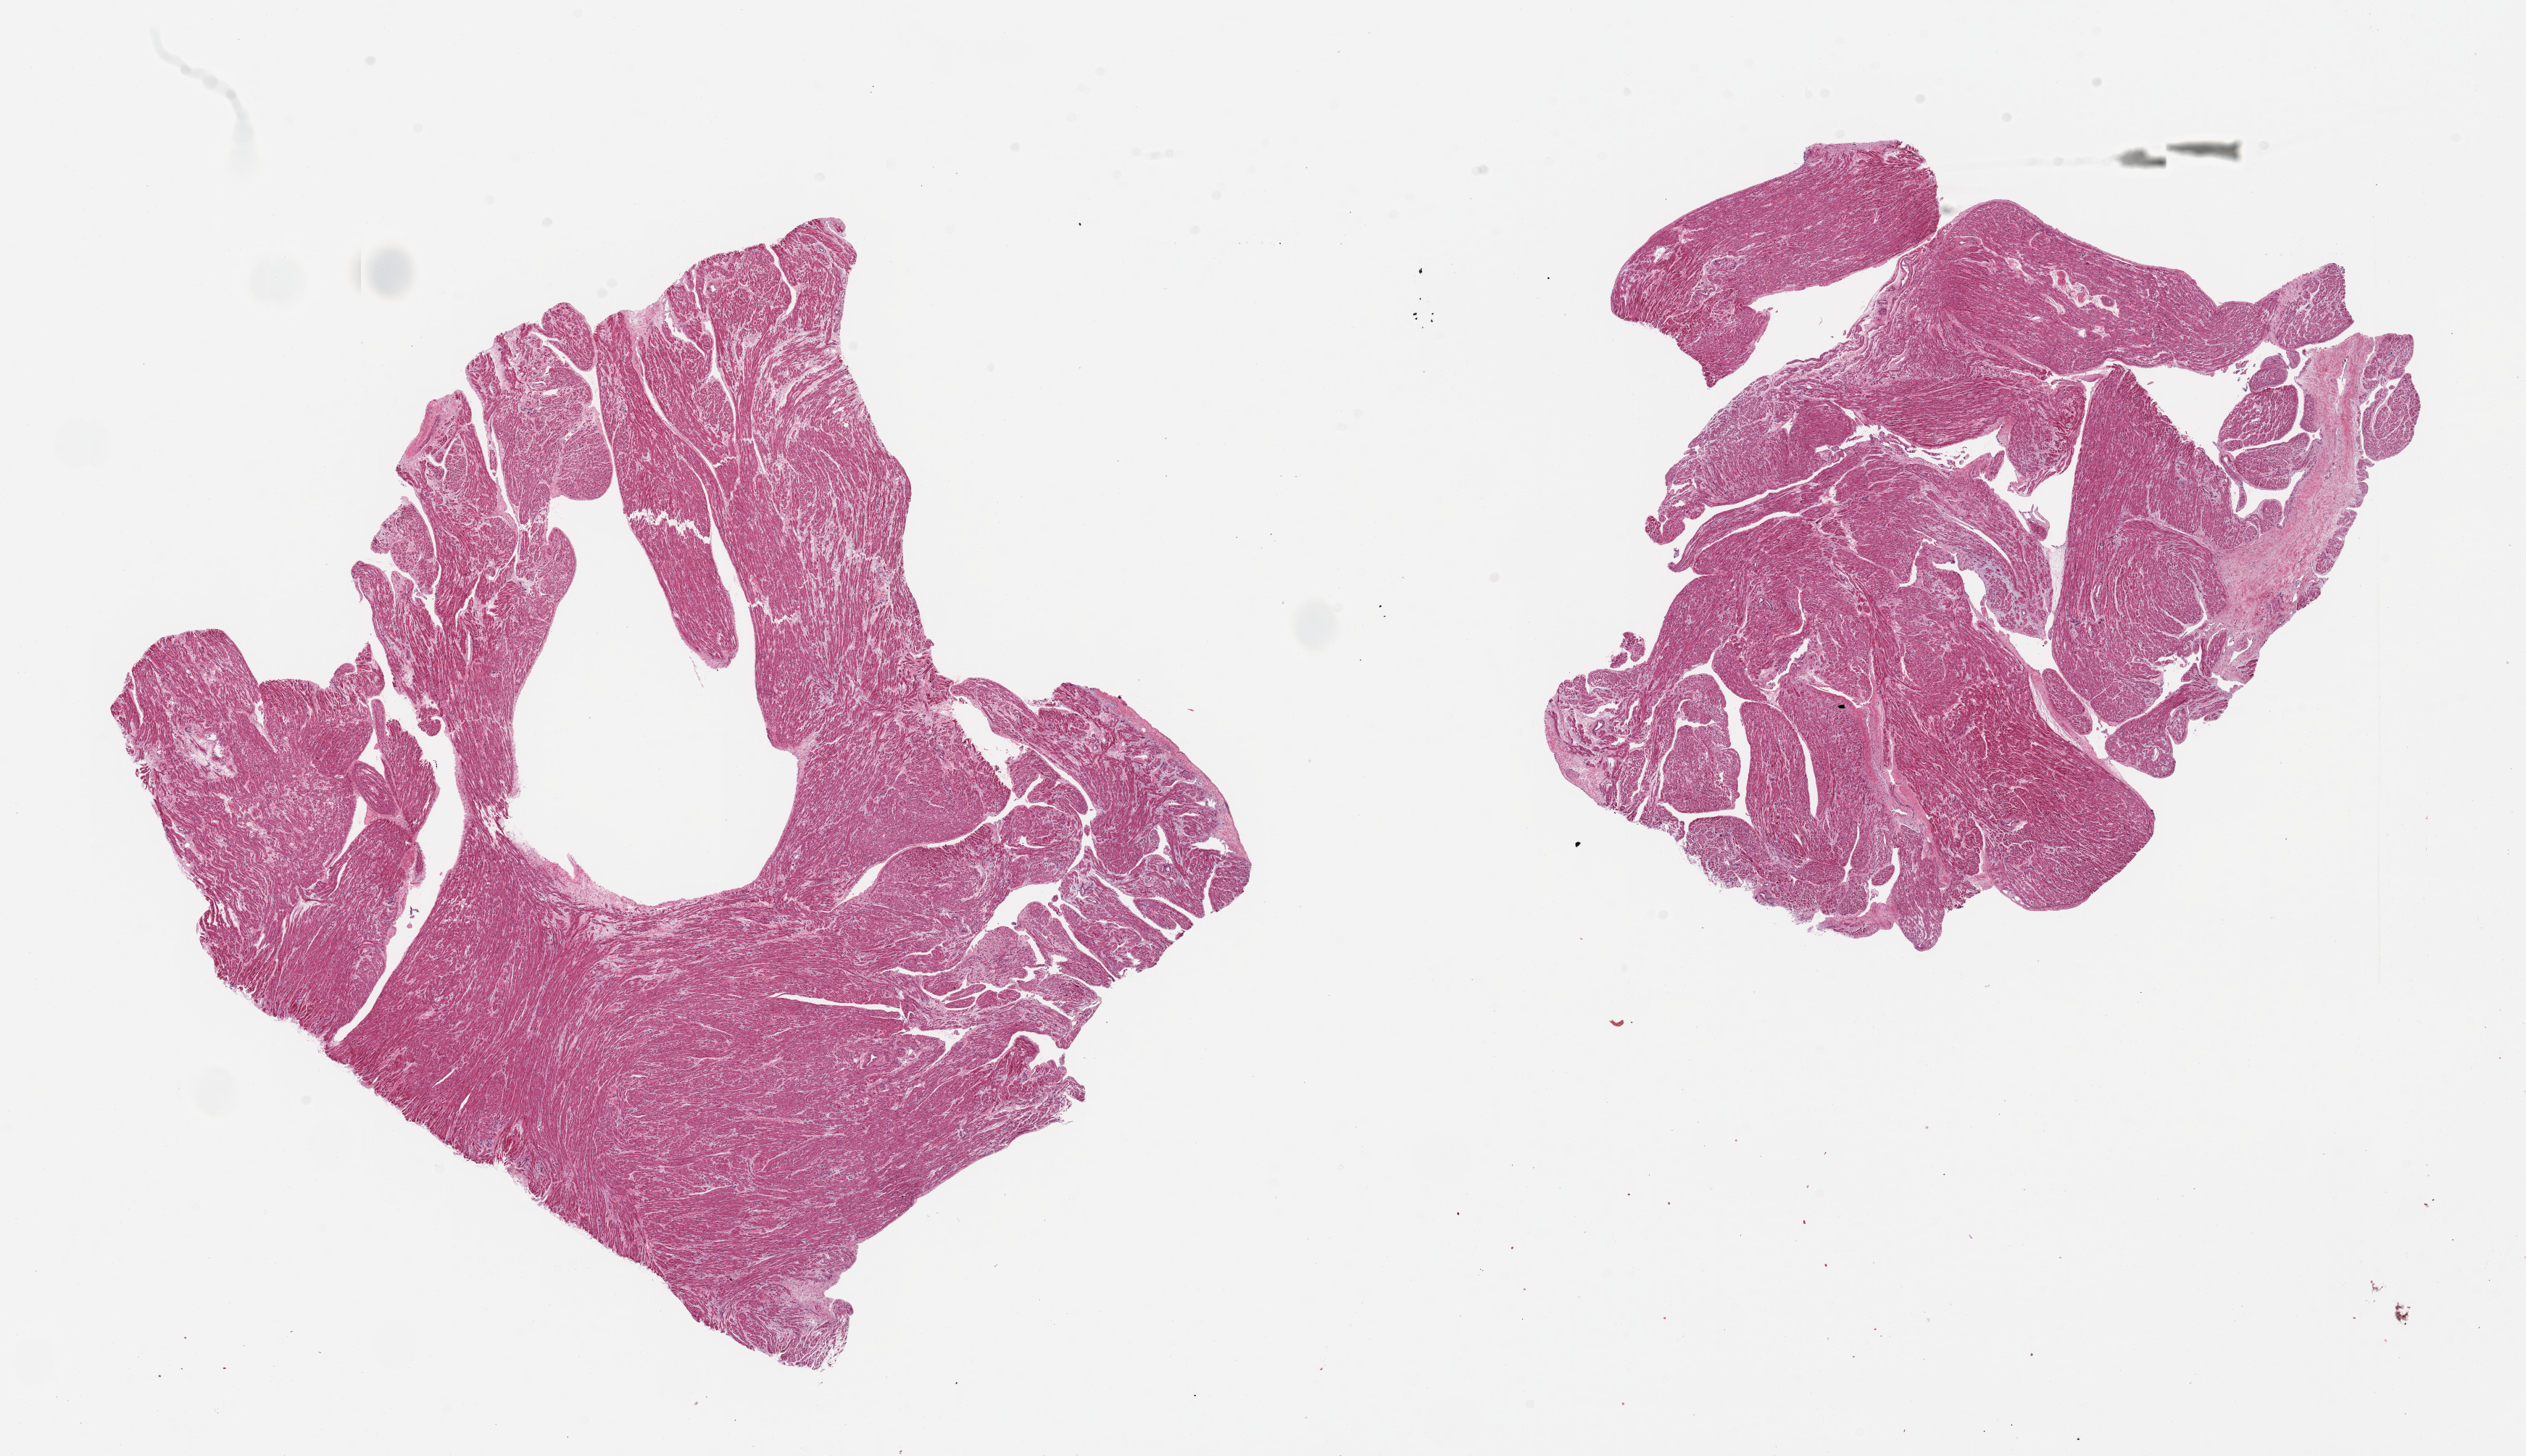
Whole-slide image, H&E stain, brightfield, whole scanned area (about 27.6 x 15.9 mm) shown as a low-resolution overview. PAXgene-fixed paraffin-embedded (PFPE) section. Section of auricular appendage (target tissue). Donor tissue sample. Donor sex: female.
Pathologist's review note for this sample: 2 pieces, 11x11 & 9x8.5mm.